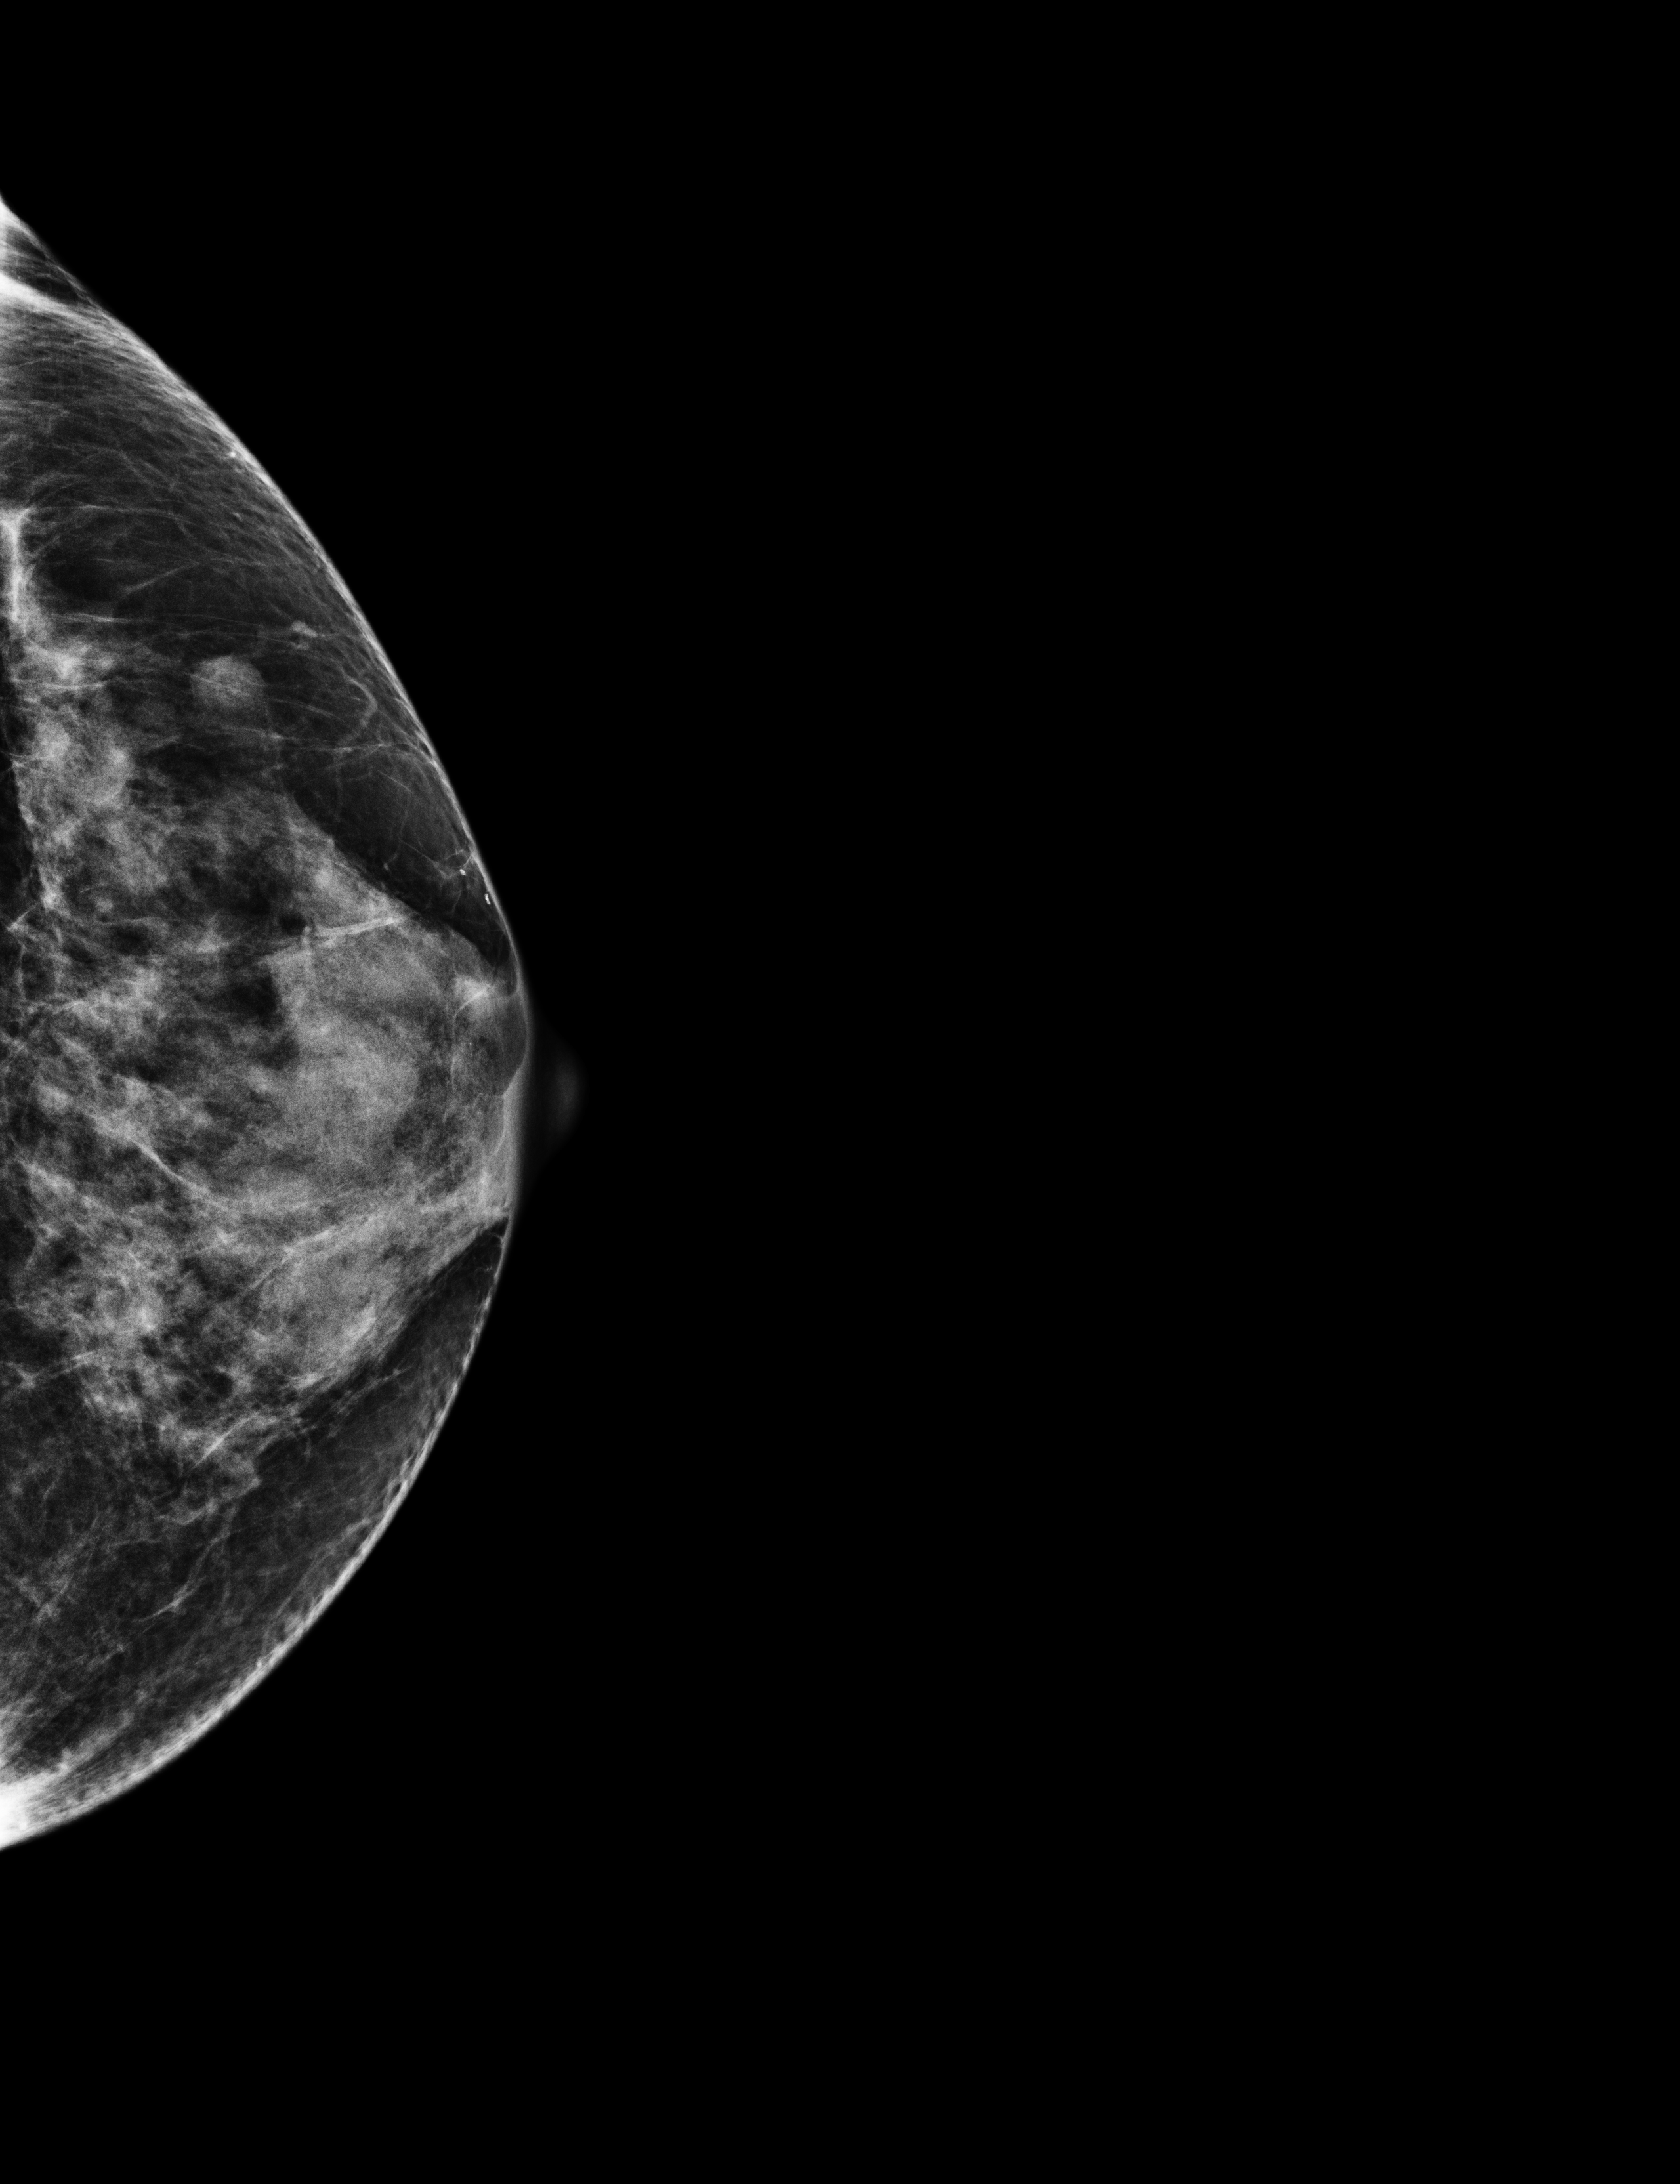
Full-field digital mammogram (FFDM), left breast, cranio-caudal projection, screening examination, system: Selenia Dimensions. Patient: female, 59 years.
- breast density at the screening exam (both breasts): heterogeneously dense (BI-RADS density category c)
- final BI-RADS assessment for this screening round (tomosynthesis exam, both breasts): category 1
- recall: no recall after this screen